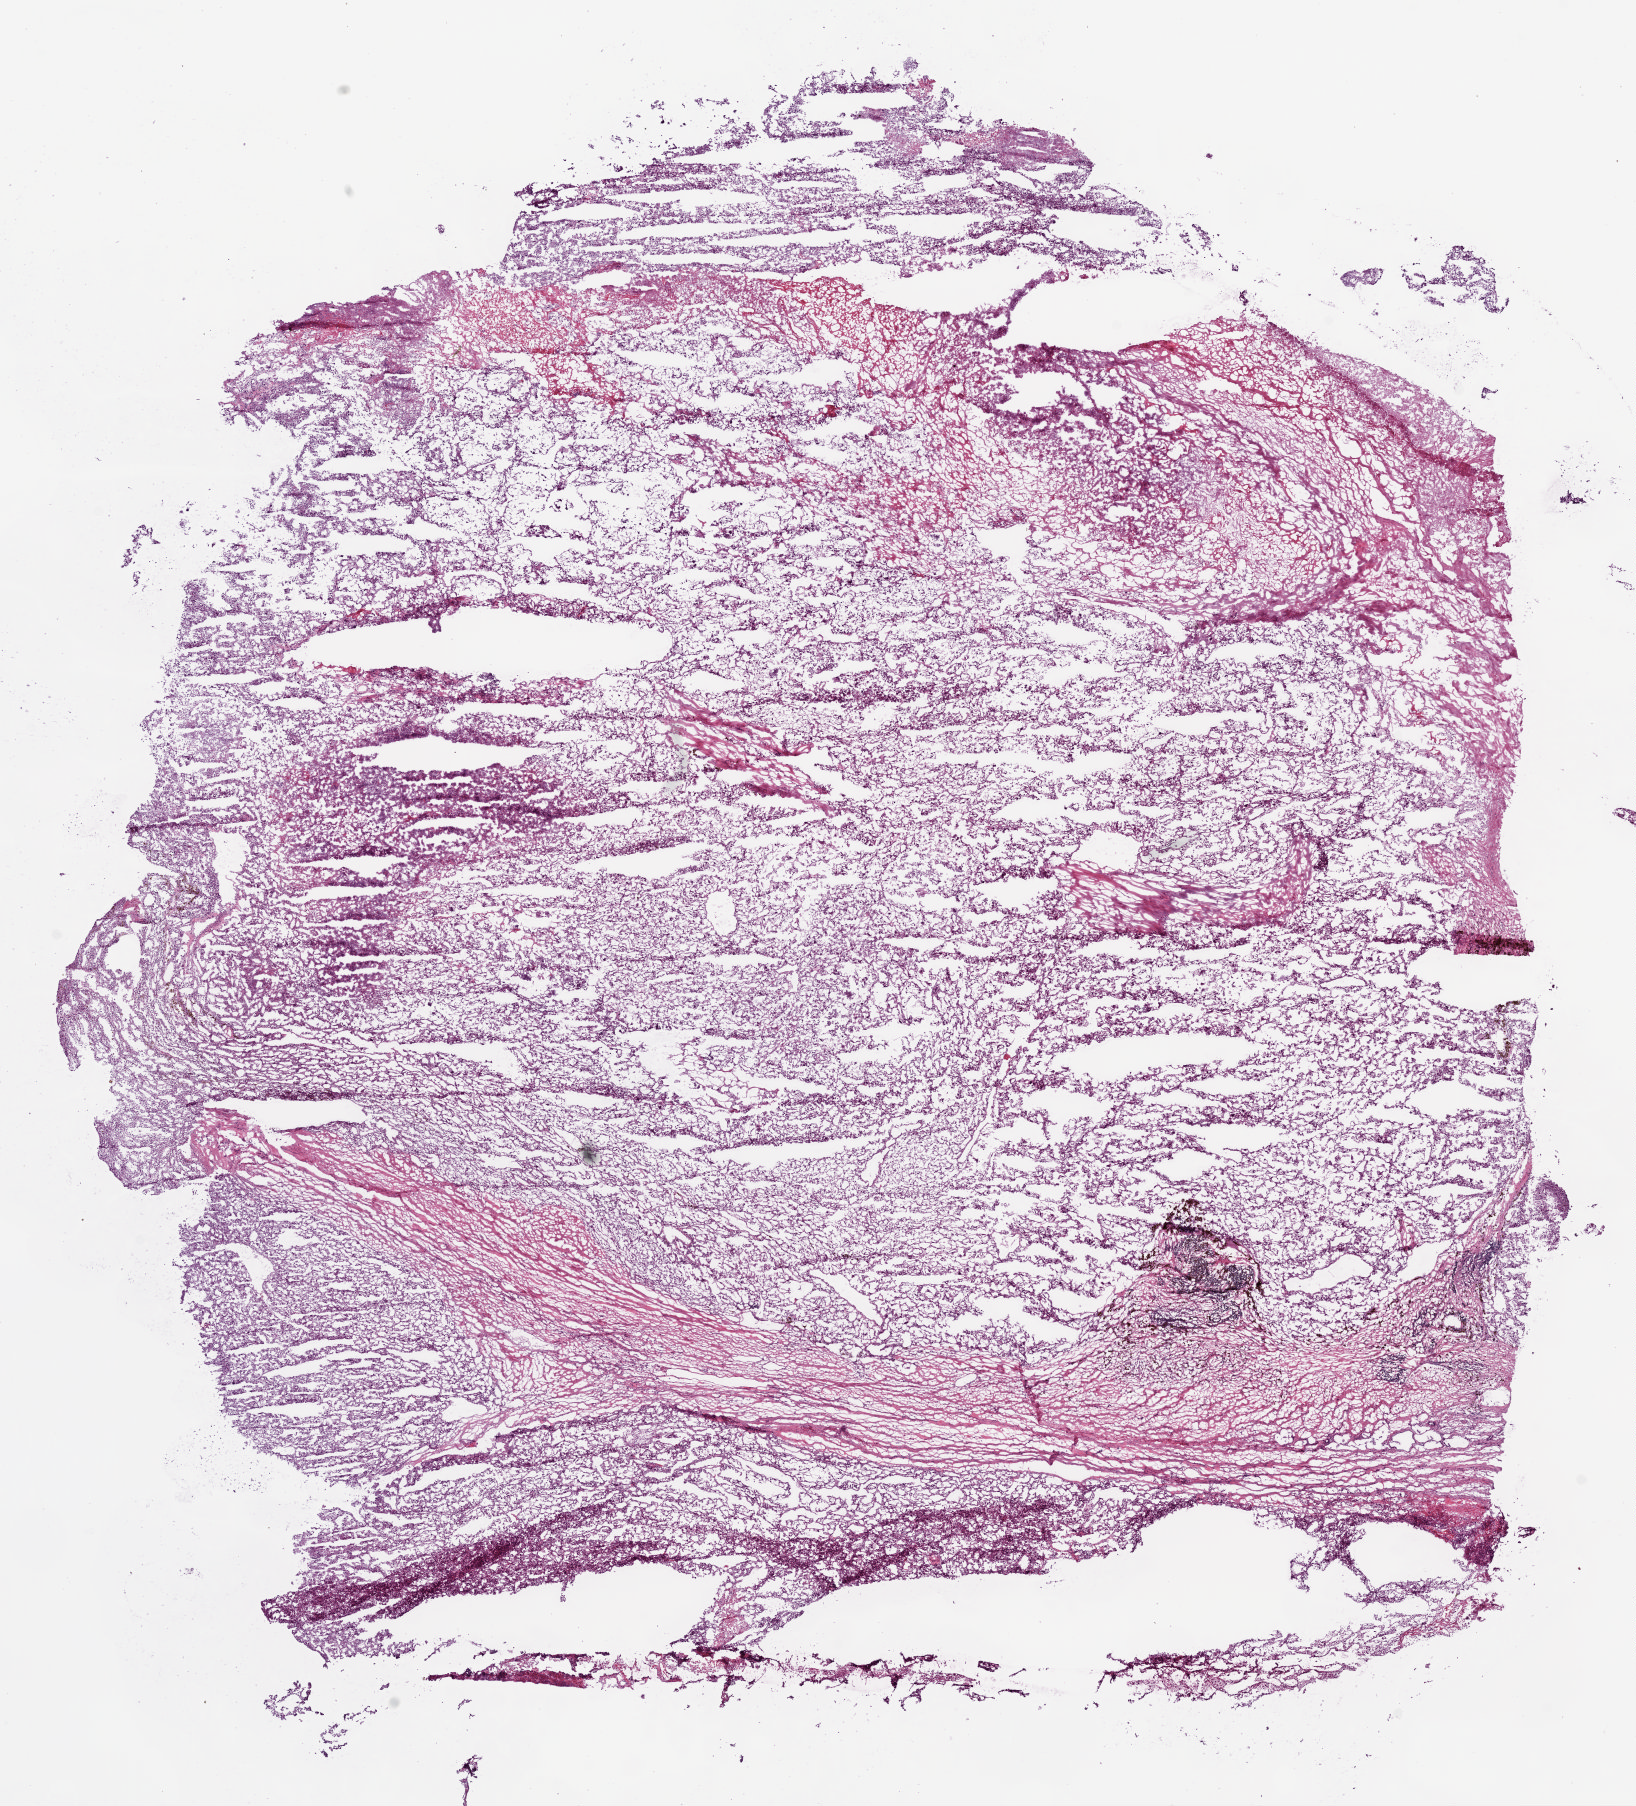
H&E whole-slide image, low-resolution overview of the scanned area, about 13.1 x 14.5 mm (from a 5x scan). Frozen section from the bottom of the tissue portion. Sample: primary tumour, kidney. Female, age 59 years at initial diagnosis. Histologic grade: G4 (undifferentiated). Slide review estimates, as recorded: tumour cells 85%, tumour nuclei 85%, normal cells 0%, stromal cells 15%, necrosis 0%.
* laterality: right
* histologic diagnosis: Clear cell adenocarcinoma, NOS
* AJCC pathologic stage: III (6th edition)